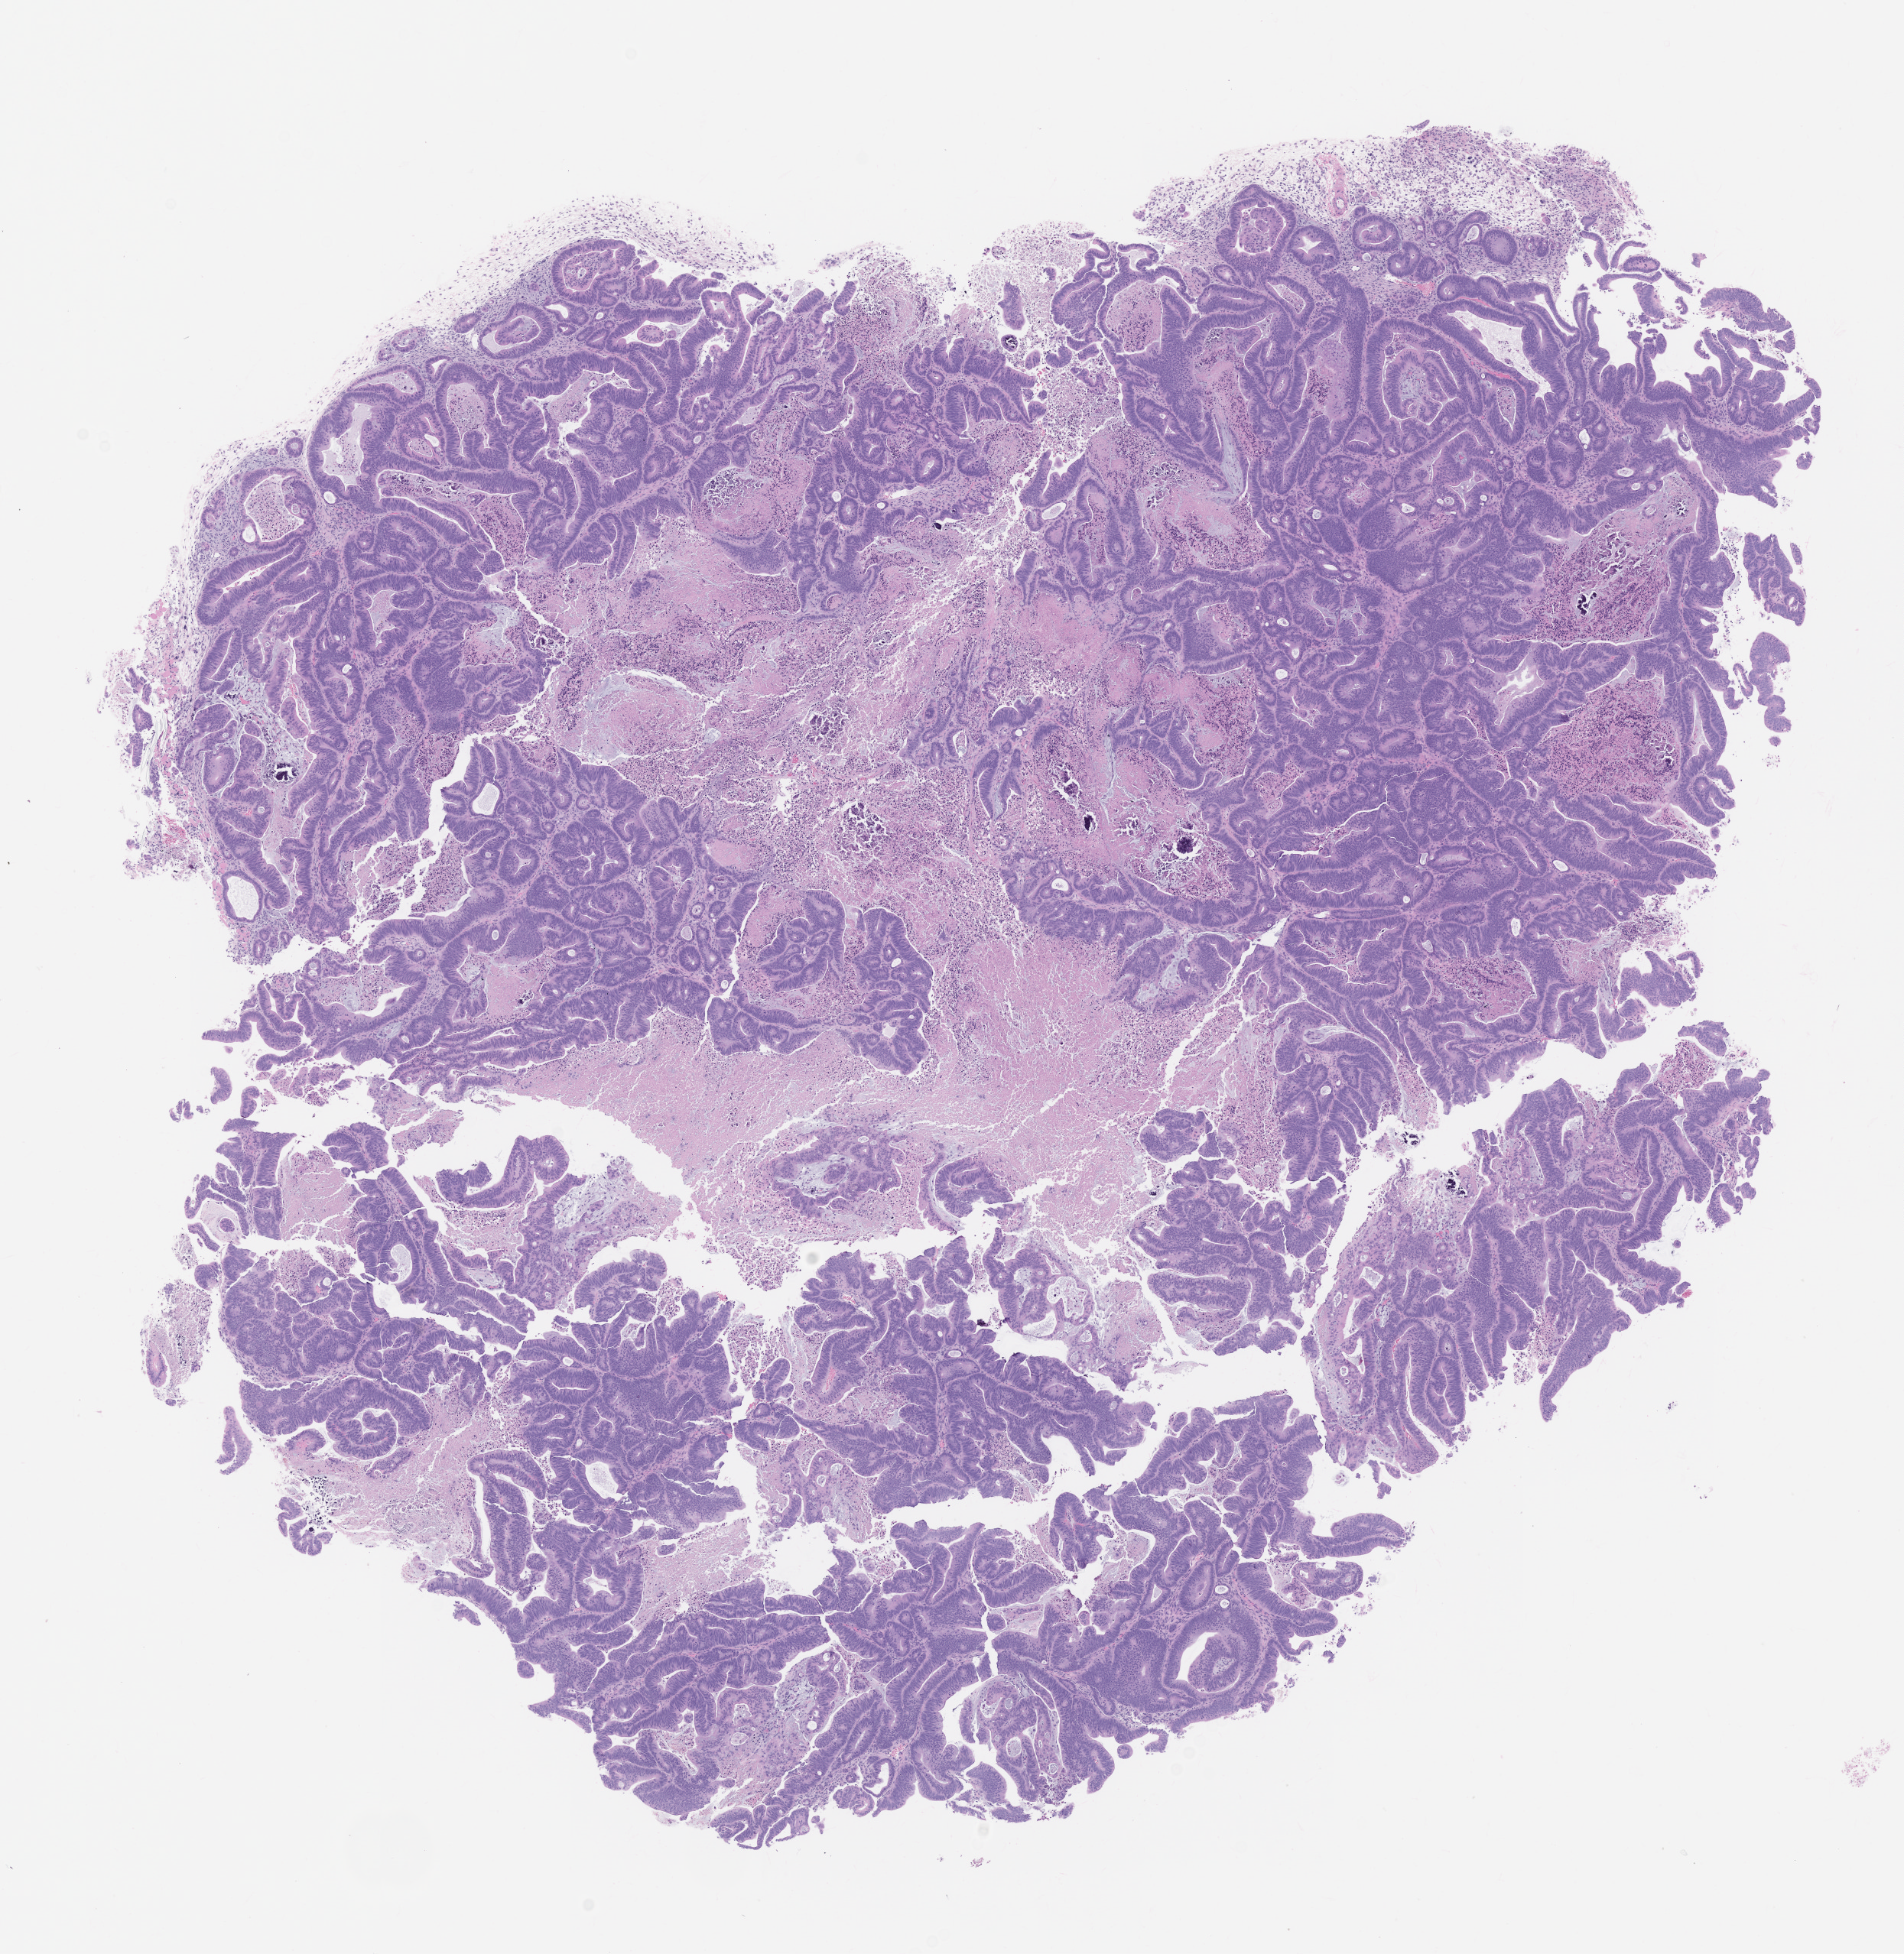
Whole-slide image, H&E: patient-derived xenograft (human tumor grown in a mouse), passage 2, a low-resolution overview of the entire scanned area, about 10.0 x 10.3 mm. Formalin-fixed paraffin-embedded section. Originating tumor site category: colon.
* originating patient diagnosis: Colon Adenocarcinoma